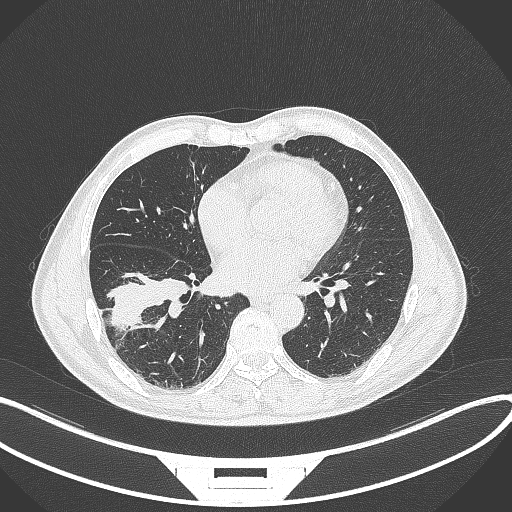
Chest CT, one axial slice. Position 155 of 364 along the scan axis. Reconstruction kernel B70f. Lung window (W 1500 / L -600 HU). 1 mm slice thickness. 512 × 512 image matrix, field of view 400 × 400 mm. Patient: male, 58 years. From the clinical record (not read from this slice): clinical TNM (as recorded): T3 N0 M0; histopathological grade: G2.
Annotated regions visible in this slice (bounding box drawn by a radiologist):
- lung tumour (recorded histology: squamous cell carcinoma): bounding box [x1, y1, x2, y2] px = [108, 268, 191, 334]